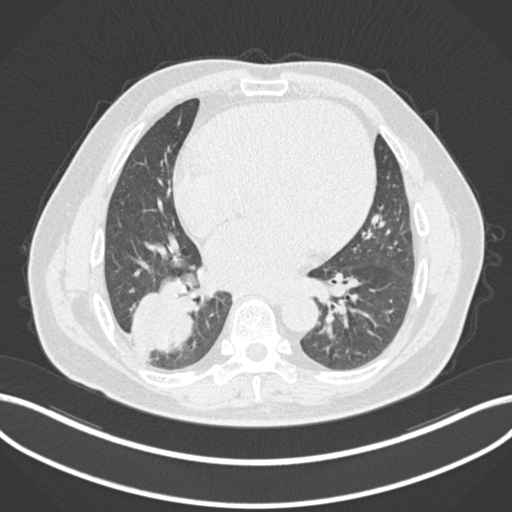
Chest CT, one axial slice; position 70 of 200 along the scan axis; reconstruction kernel B30f; lung window (W 1500 / L -600 HU); 1 mm slice thickness; 512 × 512 image matrix, field of view 400 × 400 mm. Patient: male, 59 years.
Annotated regions visible in this slice (bounding box drawn by a radiologist):
- lung tumour (recorded histology: adenocarcinoma): bounding box <126,270,195,353> (left, top, right, bottom; pixels)